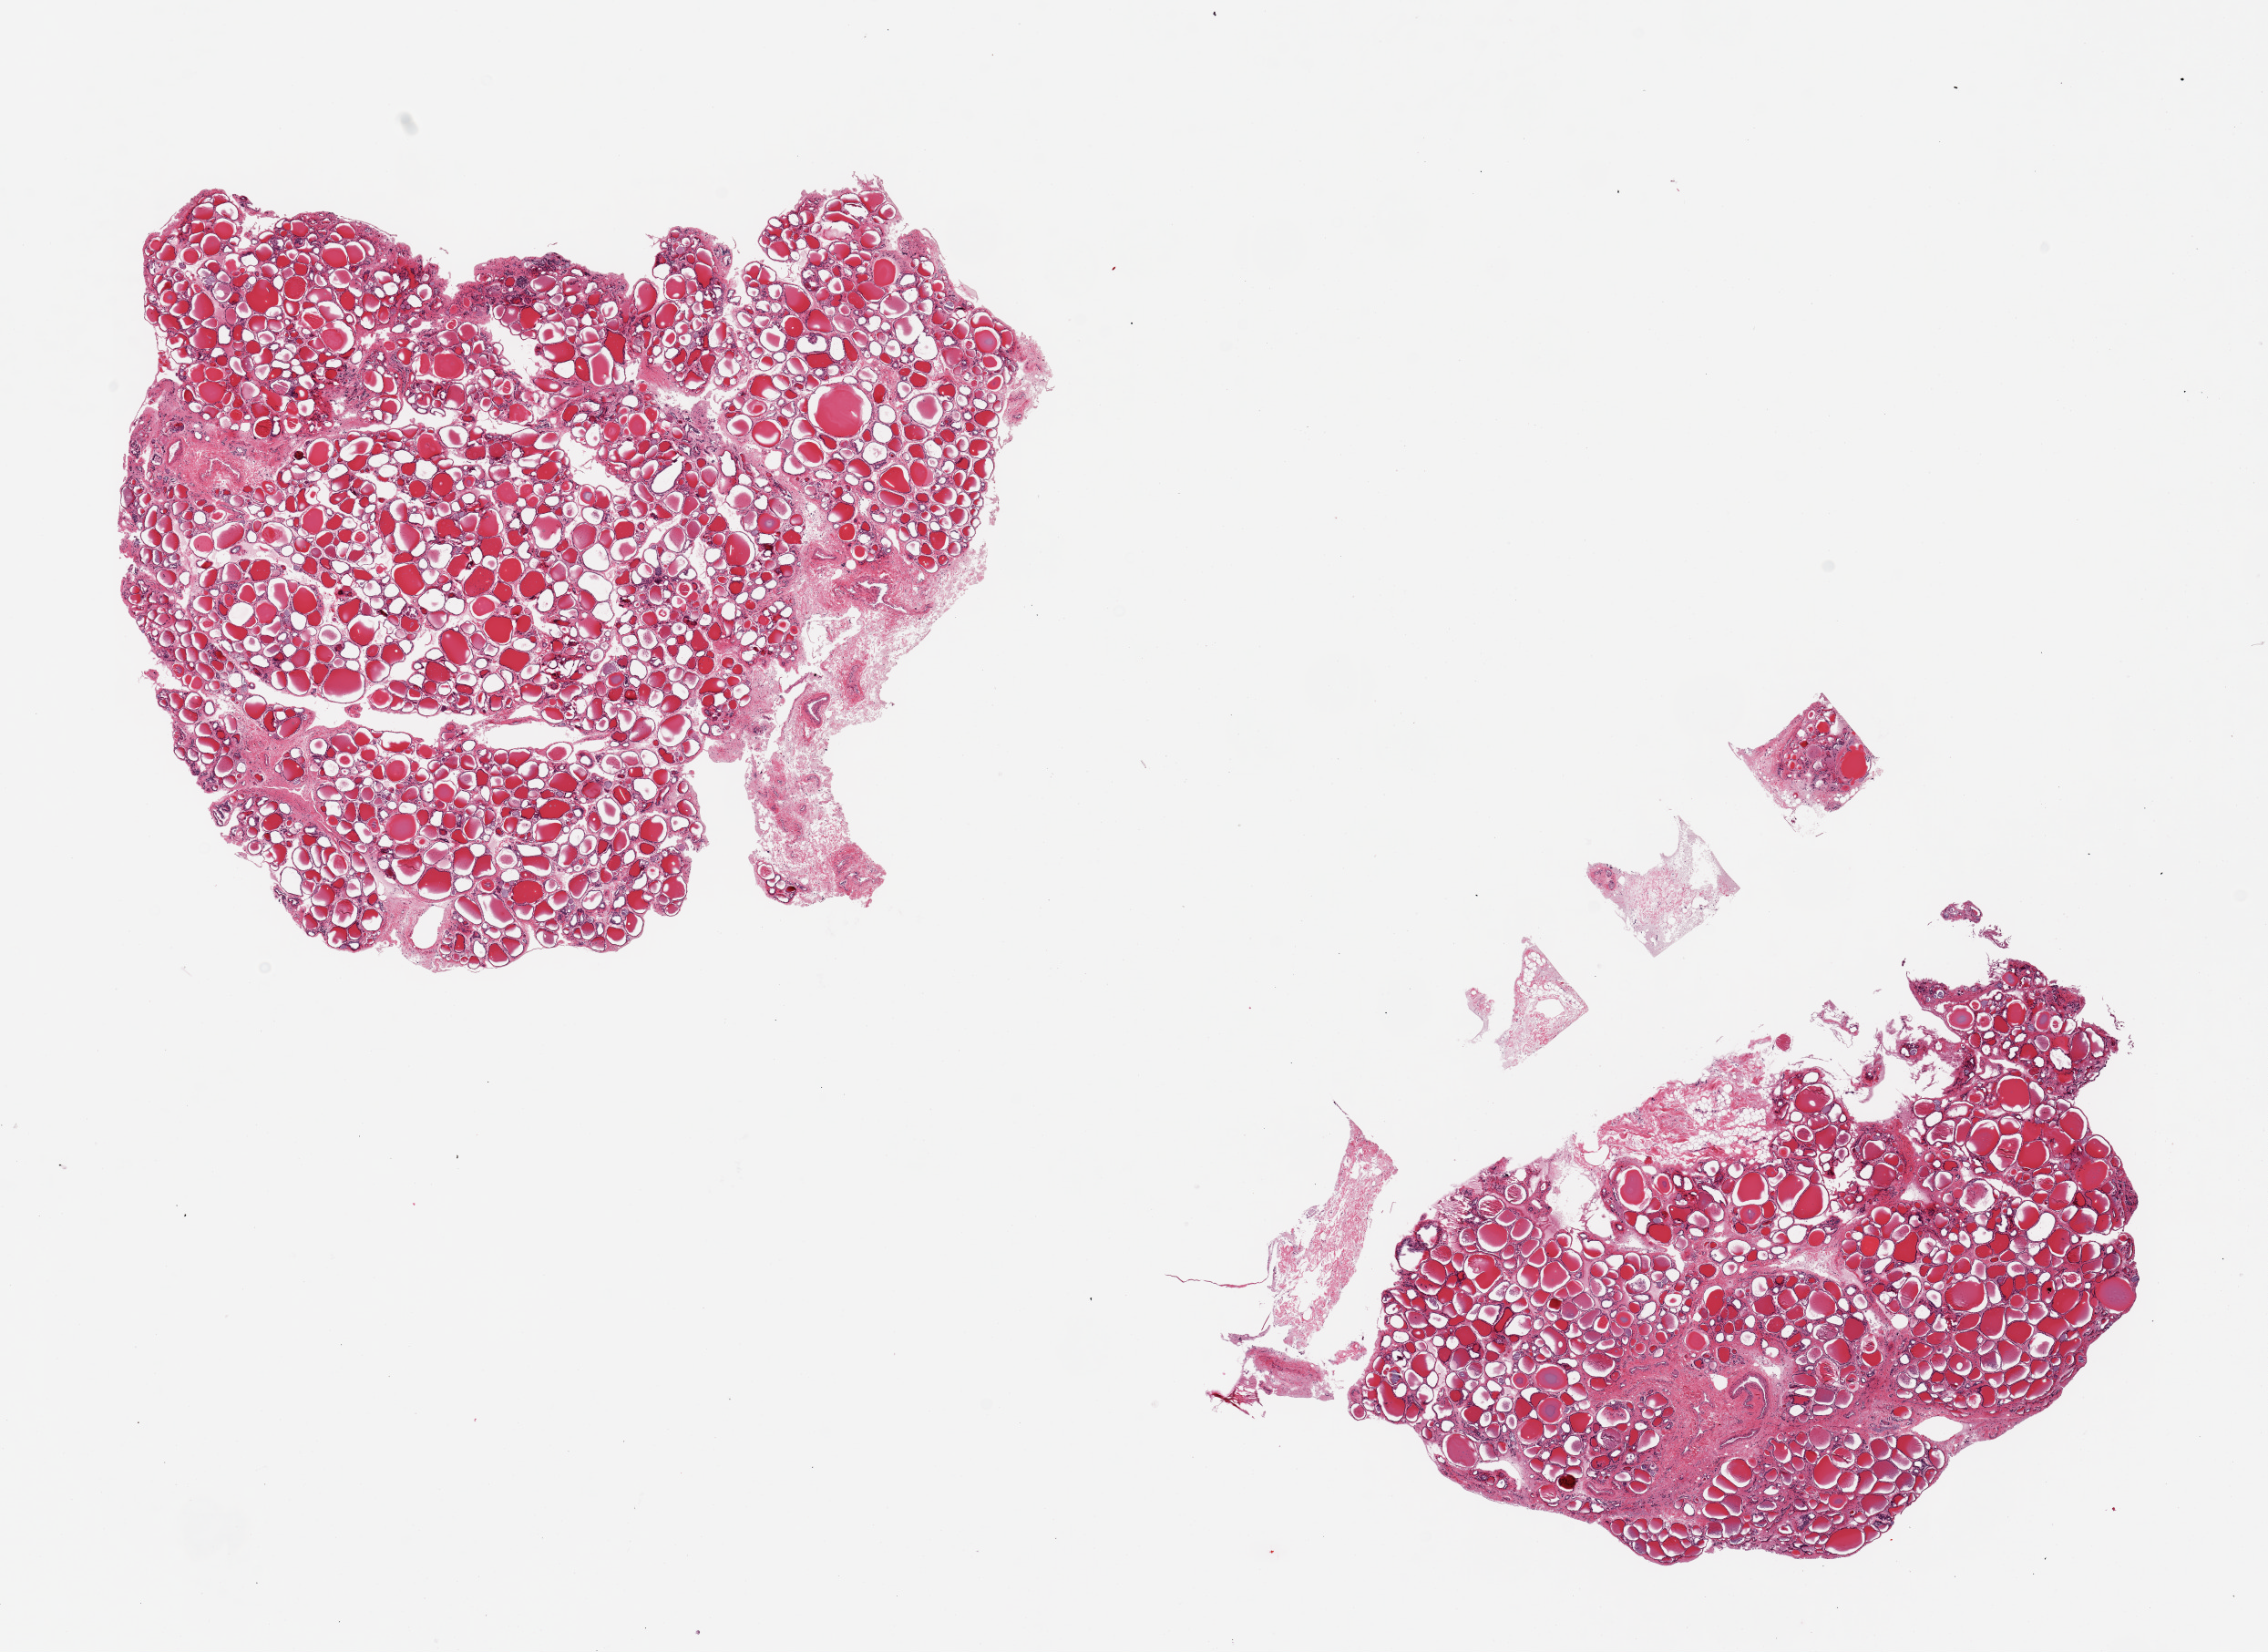
Digitized hematoxylin and eosin (H&E)-stained section — a low-resolution overview of the entire scanned area, about 19.7 x 14.3 mm (from a 20x scan). PAXgene-fixed paraffin-embedded (PFPE) section. Section of thyroid (target tissue). Tissue donor sample.
Pathologist's review note for this sample: 2 pieces, some degenerative change.